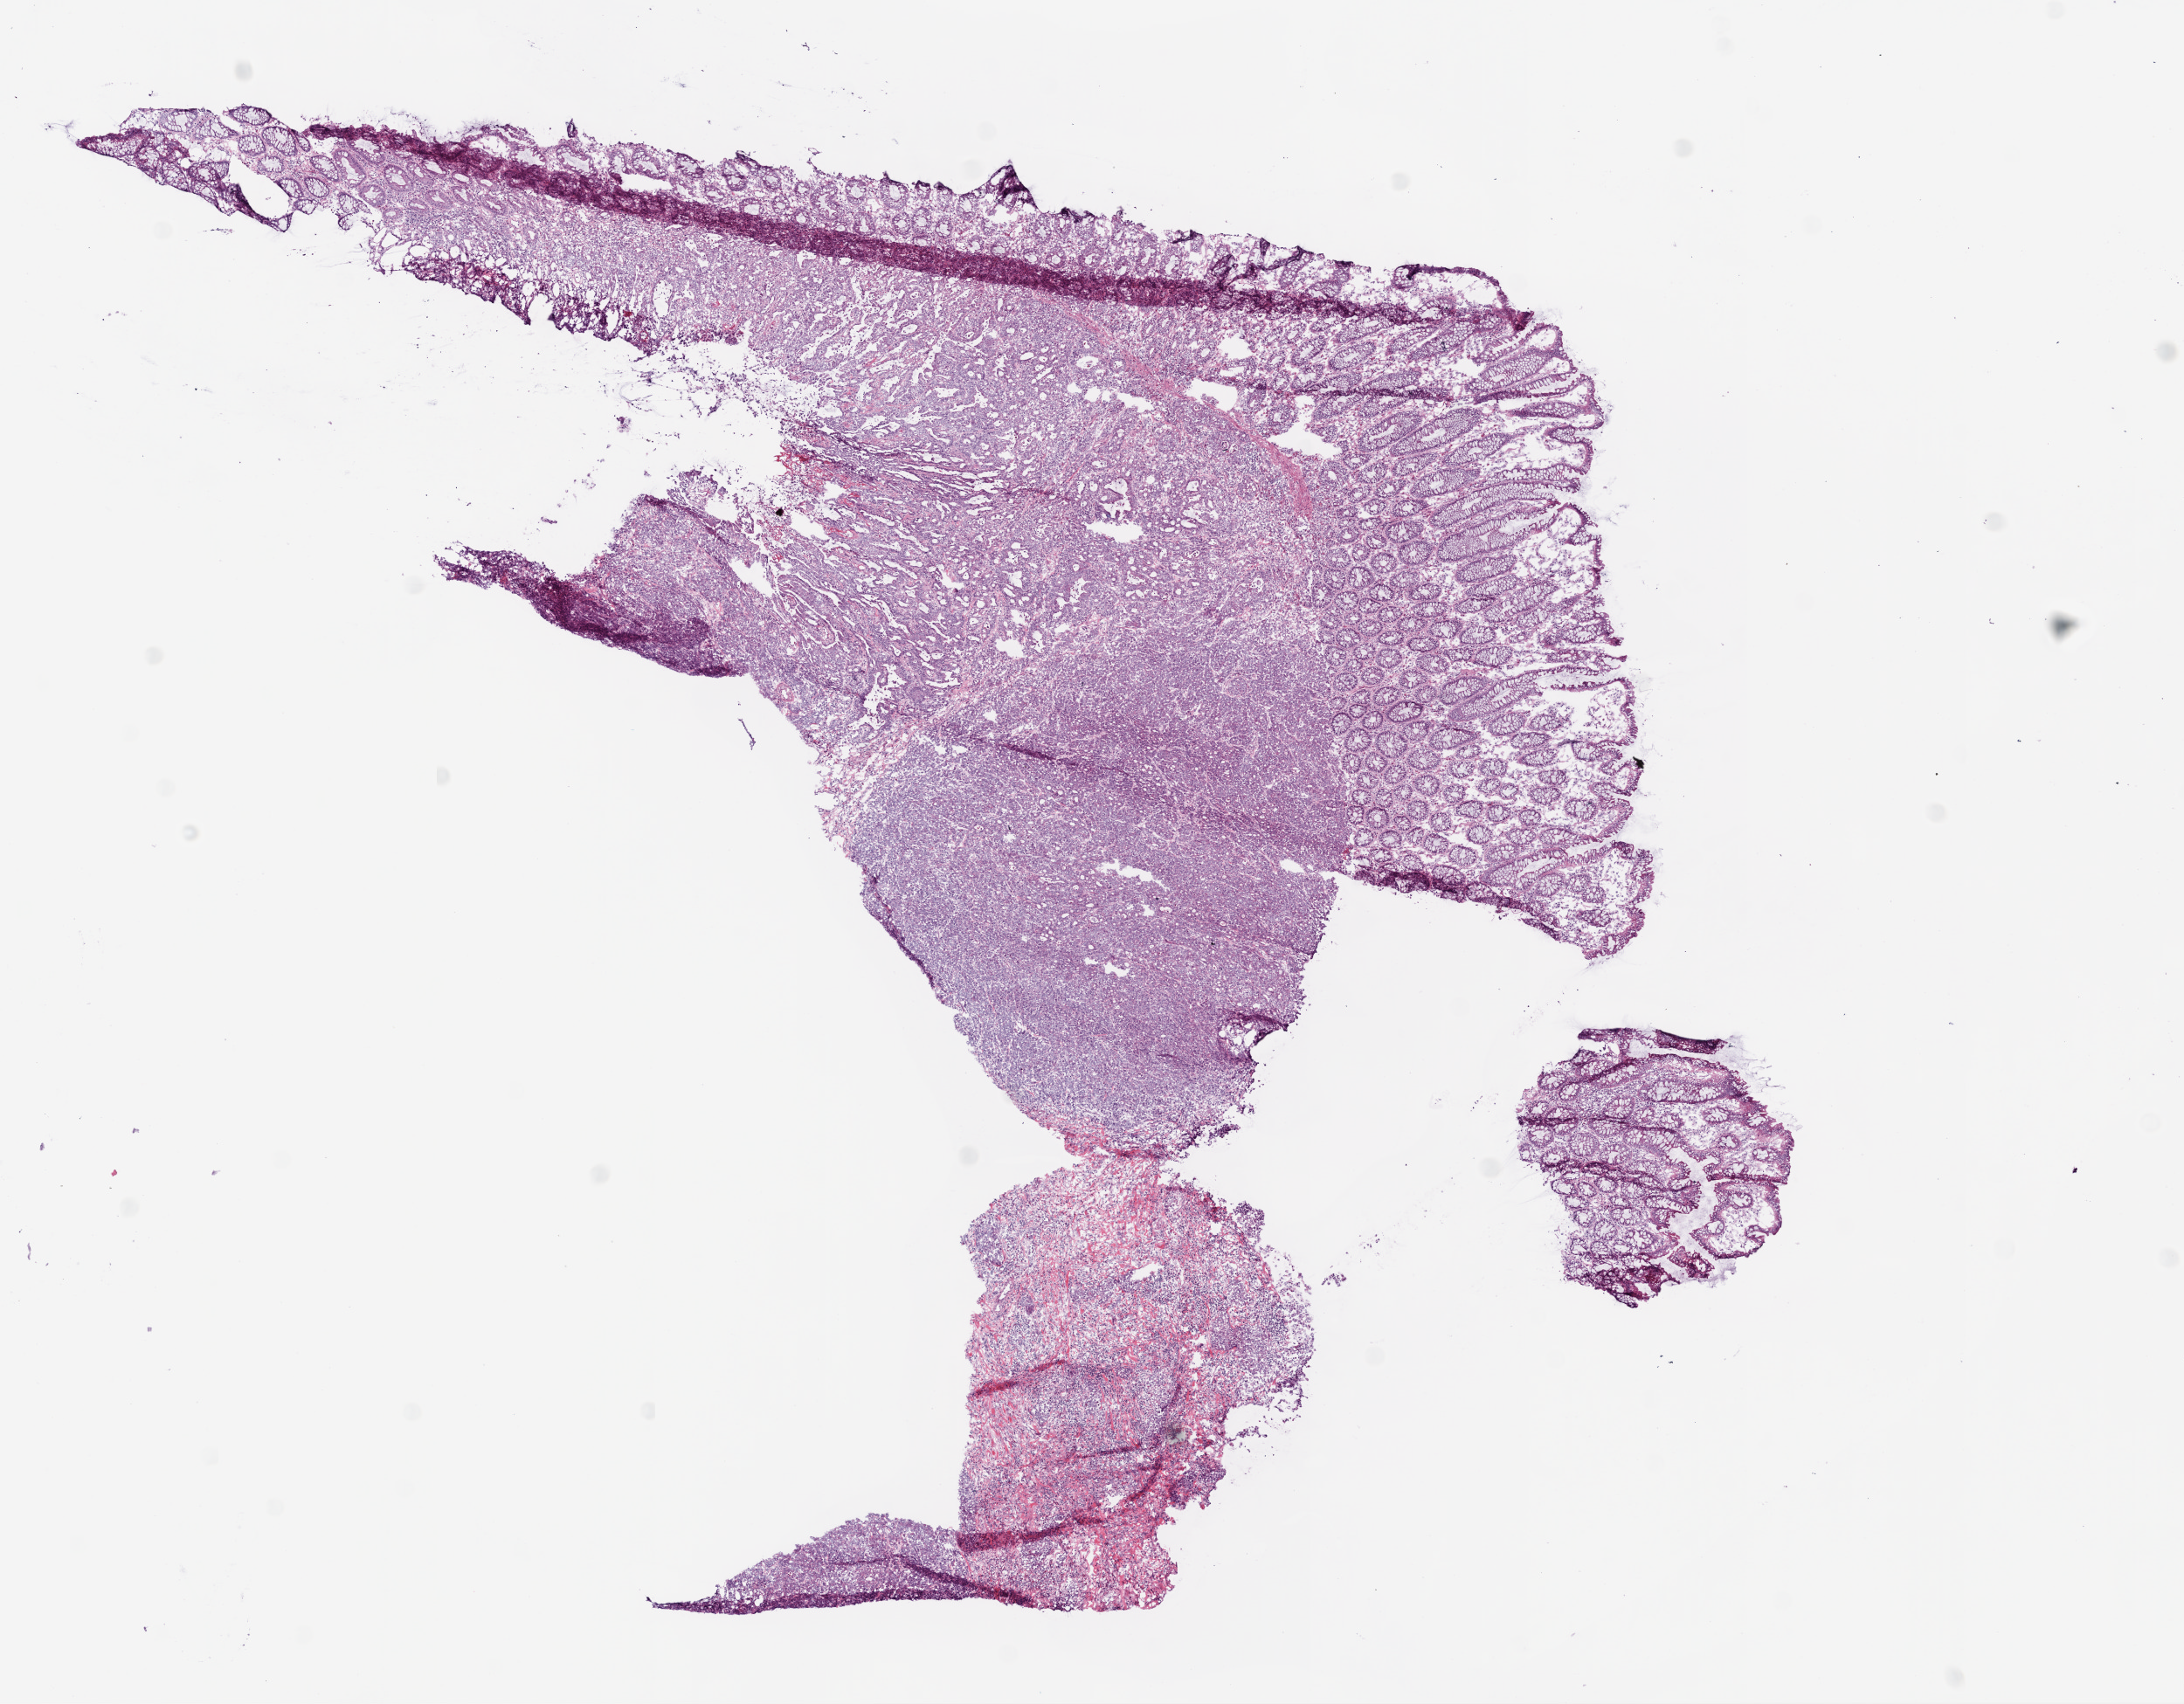
Digitized H&E tissue section (whole slide) — shown as a low-resolution overview of the whole scanned area (about 10.0 x 7.8 mm), frozen section, primary tumour sample from the colon. Patient: female, age at initial diagnosis 74 years. Pathologist review of this section (percent, as recorded): tumour cells 70%, tumour nuclei 90%, normal cells 20%, stromal cells 10%, necrosis 0%.
- pathologic diagnosis: Mucinous adenocarcinoma
- AJCC pathologic stage: III (5th edition)